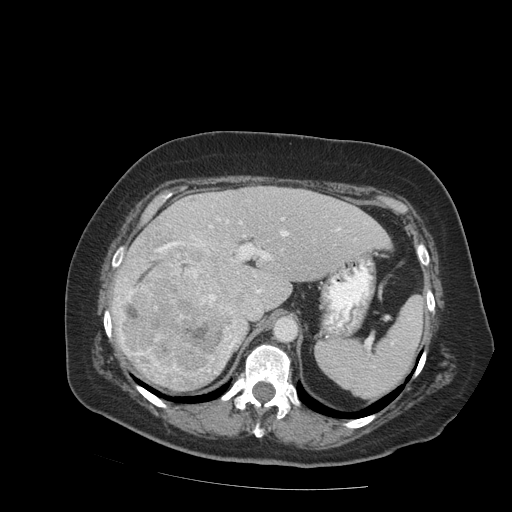
Contrast-enhanced abdominal CT (liver protocol), one axial slice; 140 kVp; soft-tissue window (W 400 / L 40 HU); 2.5 mm slice thickness; 512 × 512 image matrix. From the clinical record (not read from this slice): diagnosis: hepatocellular carcinoma (patient treated with transarterial chemoembolisation; whether this scan precedes or follows treatment is not stated here); TNM stage (as recorded): Stage-IVB; Child-Pugh class: A; tumour nodularity: uninodular.
Outlined on this slice (semi-automatic segmentation, software-assisted and operator-edited):
- liver parenchyma outside the tumour (the mass and vessels are separate outlines, so this box may not span the whole liver): bounding box <112,186,390,392> (left, top, right, bottom; pixels)
- mass: <115,226,242,388>
- liver vessels: <191,217,340,293>